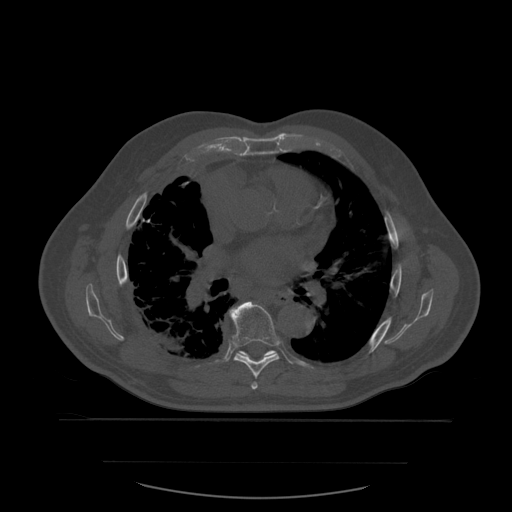
CT including the spine, one axial slice; slice 380 of 590 in the series (ordered by position); bone window (W 1800 / L 400 HU); 1.25 mm slice thickness; 512 × 512 image matrix, field of view 479 × 479 mm. Patient age 71 years. Case-level facts recorded for this patient, not image findings: primary cancer: lung.
Annotated regions visible in this slice (semi-automatic segmentation, software-assisted and operator-edited):
- T6 vertebra: bounding box <251,382,258,390> (left, top, right, bottom; pixels)
- T7 vertebra: <229,301,280,379>
- T8 vertebra: <241,351,274,358>